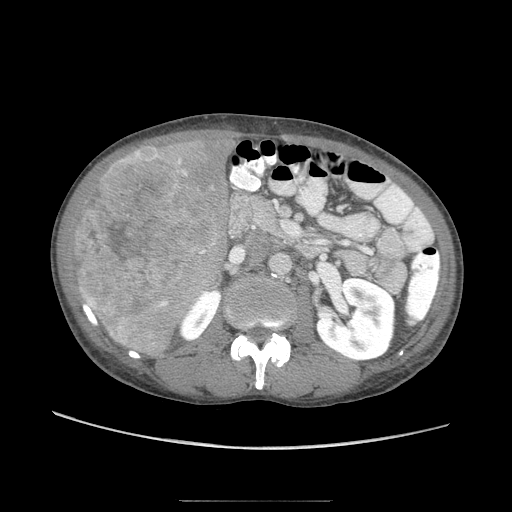
Contrast-enhanced abdominal CT (liver protocol), one axial slice. Position 28 of 103 along the scan axis. Reconstruction kernel STANDARD. Soft-tissue window (W 400 / L 40 HU). 2.5 mm slice thickness. 512 × 512 image matrix, field of view 380 × 380 mm. Case-level facts recorded for this patient, not image findings: diagnosis: hepatocellular carcinoma (patient treated with transarterial chemoembolisation; whether this scan precedes or follows treatment is not stated here); TNM stage (as recorded): Stage-IIIA; Child-Pugh class: A; tumour differentiation: moderately differentiated; tumour size: 16 cm.
Annotated regions visible in this slice (semi-automatically segmented with operator editing):
- liver parenchyma outside the tumour (the mass and vessels are separate outlines, so this box may not span the whole liver): bounding box <92,130,236,360> (left, top, right, bottom; pixels)
- mass: <68,144,217,340>